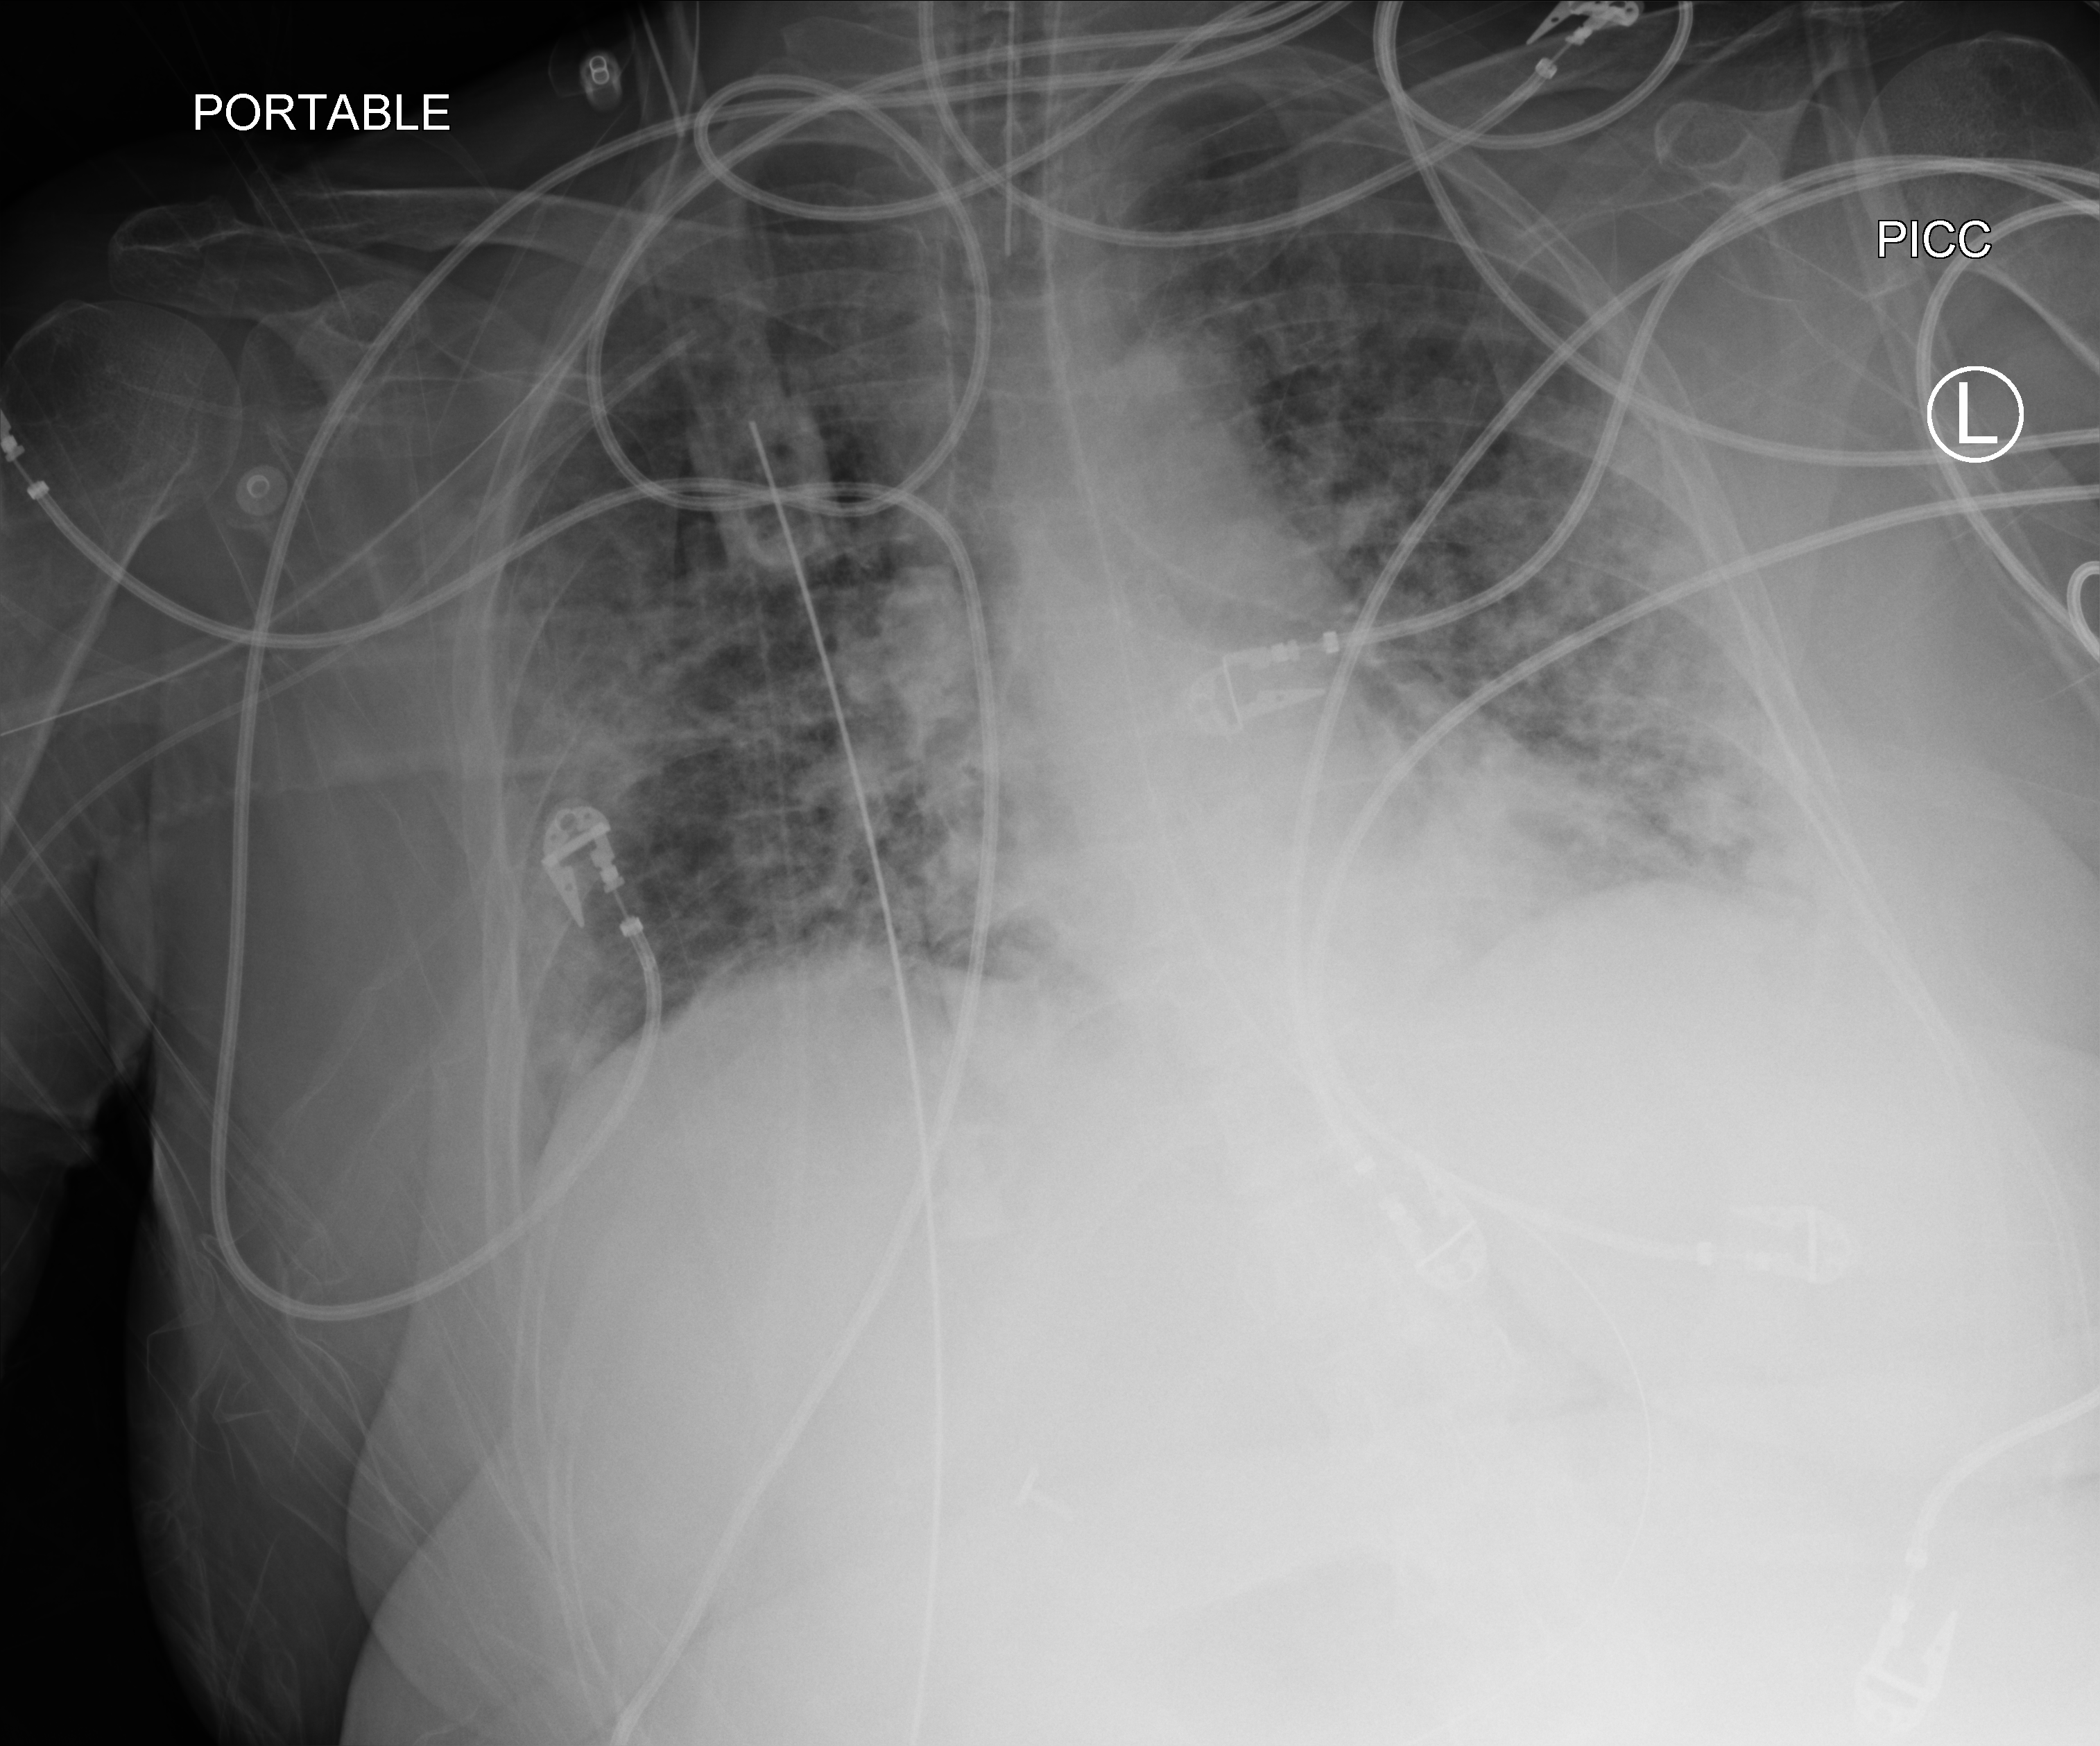
Bedside chest radiograph (computed radiography). Patient hospitalised with COVID-19; female, aged 18–59 years.
From the hospital-stay record, not from the radiograph (when in the stay this image was taken is not recorded): admitted to intensive care during this hospital stay: yes; mechanically ventilated during this hospital stay: yes.